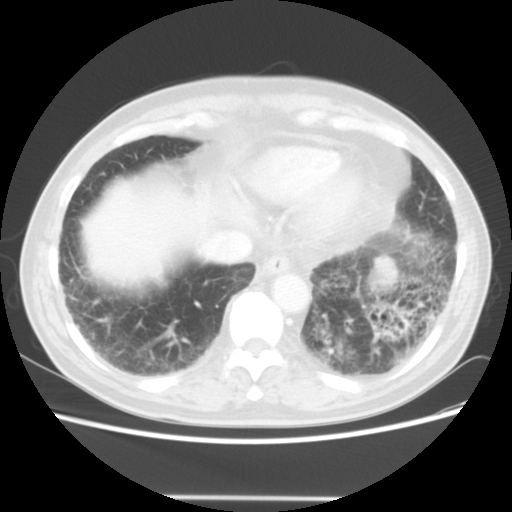
Chest CT, one axial slice; position 11 of 56 along the scan axis; lung window (W 1500 / L -600 HU); 5 mm slice thickness; 512 × 512 image matrix, field of view 360 × 360 mm. Male patient, age 66 years. From the clinical record (not read from this slice): clinical TNM (as recorded): T4 N3 M0.
Outlined on this slice (bounding box drawn by a radiologist):
- lung tumour (recorded histology: small cell carcinoma): bounding box [x1, y1, x2, y2] px = [364, 240, 402, 287]